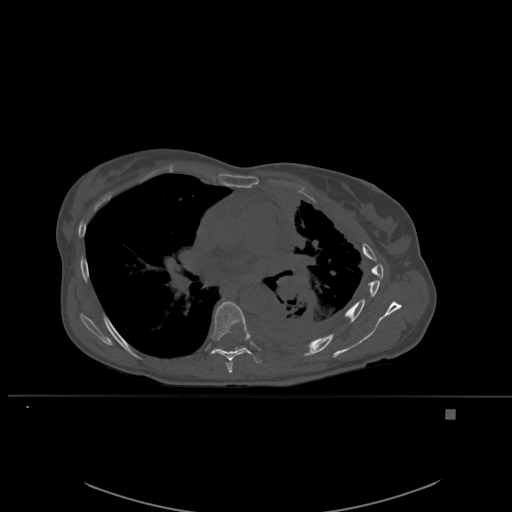
CT including the spine, one axial slice. Position 366 of 537 along the scan axis. Bone window (W 1800 / L 400 HU). 512 × 512 image matrix. Patient: female, 45 years. From the clinical record (not read from this slice): primary cancer: lung.
Structures marked on this image (semi-automatically segmented with operator editing):
- T6 vertebra: bounding box [x1, y1, x2, y2] px = [226, 359, 233, 373]
- T7 vertebra: [205, 301, 262, 364]
- T8 vertebra: [235, 346, 244, 351]